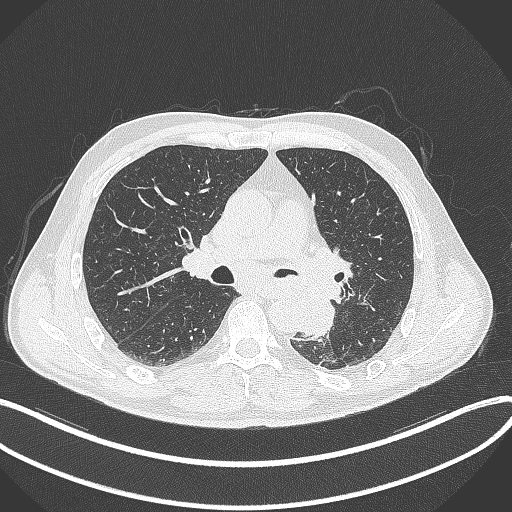
Chest CT, one axial slice; position 201 of 329 along the scan axis; 120 kVp; lung window (W 1500 / L -600 HU); 1 mm slice thickness; 512 × 512 image matrix. Patient: male, 59 years. Case-level facts recorded for this patient, not image findings: clinical TNM (as recorded): T2a N2 M0.
Annotated regions visible in this slice (rectangle marked by the reading radiologist):
- lung tumour (recorded histology: squamous cell carcinoma): bounding box (x1, y1, x2, y2) in pixels: (293, 287, 339, 341)